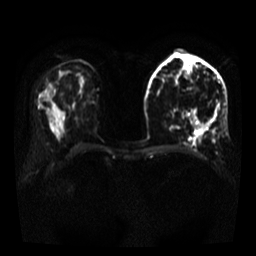
Breast MRI, one axial slice; slice 19 of 35 in the series (ordered by position); diffusion-weighted series; image 2 of 4 stored at this slice position (different b-values; order by instance number); 3 T; 5 mm slice thickness; 256 × 256 image matrix, field of view 320 × 320 mm. Female patient.
Annotated regions visible in this slice (expert manual segmentation):
- tumour on diffusion-weighted imaging: box from (x=191, y=114) to (x=200, y=131) px